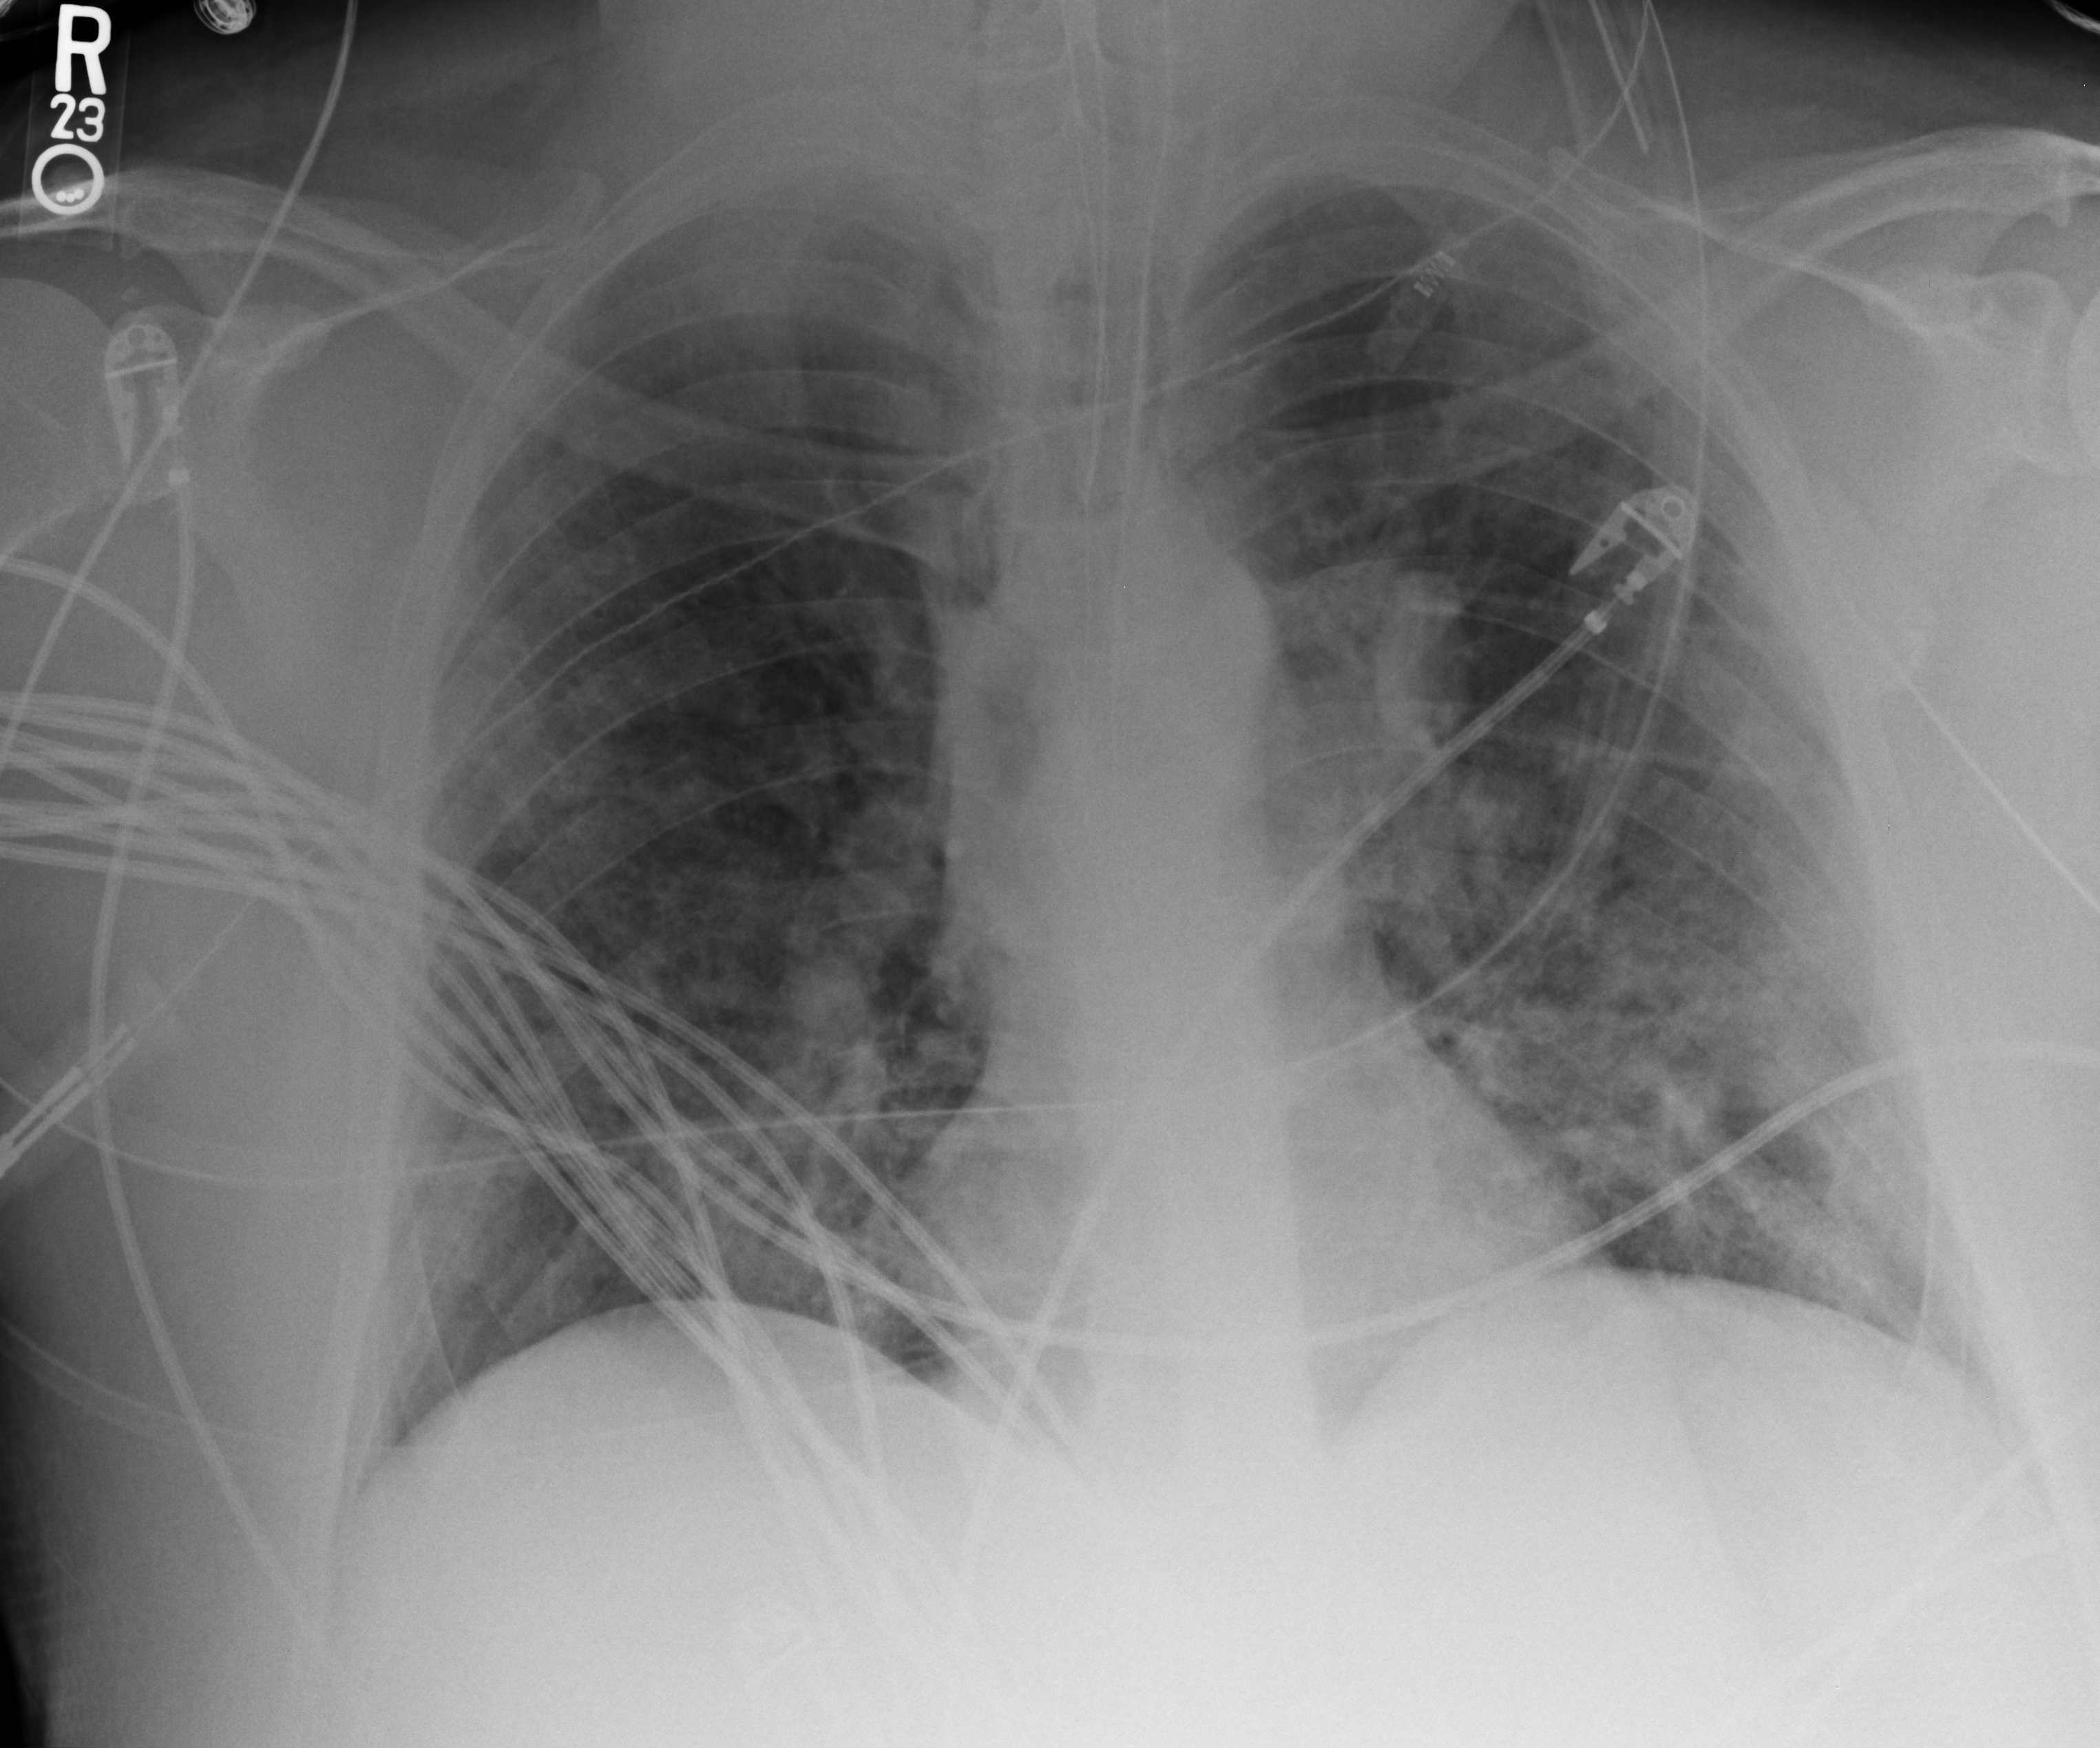
Chest X-ray (portable), anteroposterior (AP) projection. Adult patient hospitalised with COVID-19, age 18–59 years.
Admission-level facts for this patient (not findings on this image; timing relative to this image not recorded):
- mechanically ventilated during this hospital stay: yes
- diabetes (admission record): no